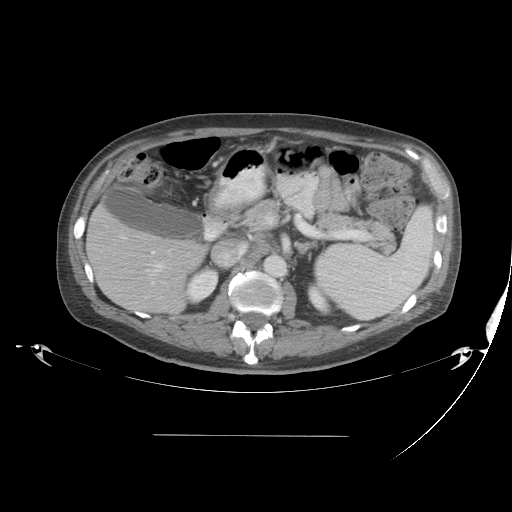
Contrast-enhanced abdominal CT, one axial slice; slice 22 of 48 in the series (ordered by position); 120 kVp; intravenous contrast given; soft-tissue window (W 400 / L 40 HU); 5 mm slice thickness; 512 × 512 image matrix. Male patient, age 65 years. From the clinical record (not read from this slice): diagnosis: colorectal cancer liver metastases, imaged before liver resection.
Outlined on this slice (expert manual segmentation):
- hepatic veins: bounding box <151,251,164,284> (left, top, right, bottom; pixels)
- liver: <88,208,205,314>
- portal vein (with intrahepatic branches): <118,234,150,272>